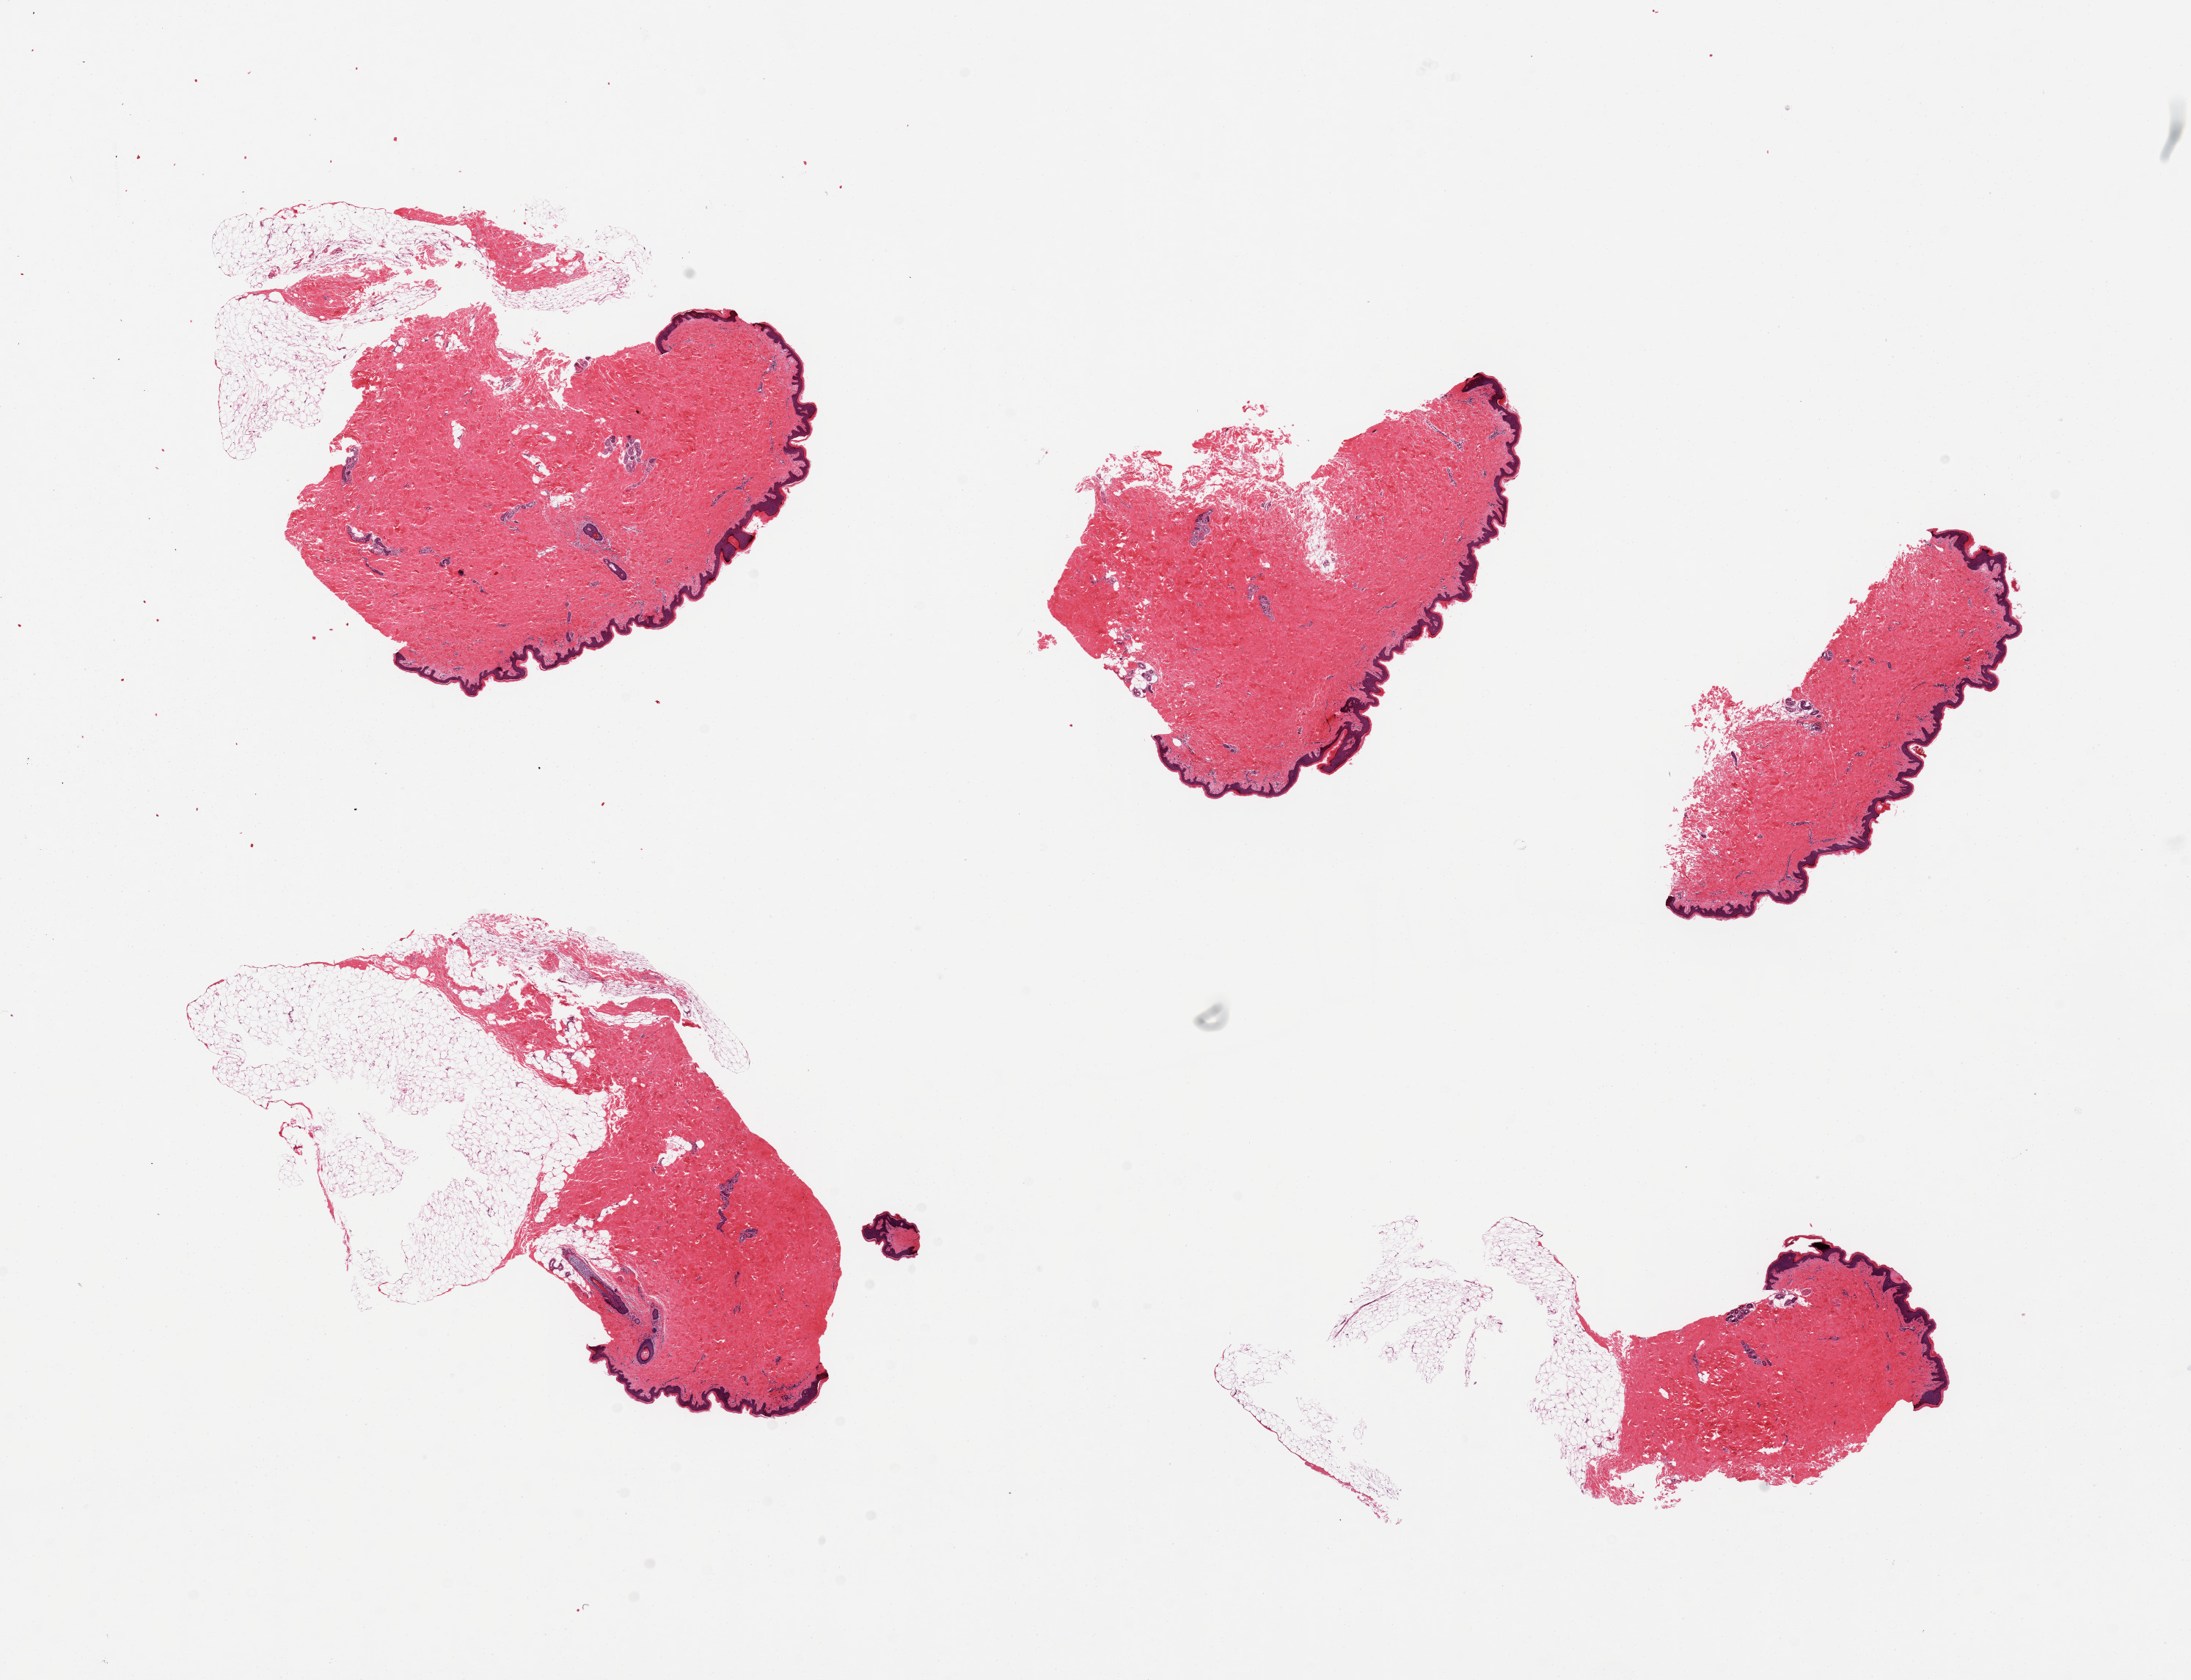
Digitized haematoxylin and eosin-stained section — low-resolution overview of the scanned area, about 23.6 x 18.1 mm (from a 20x scan), PAXgene-fixed paraffin-embedded (PFPE) section, target tissue: skin of suprapubic region, tissue donor sample. Donor sex: female.
Reviewer comment on this tissue sample: 5 pieces, 3 of 5 include significant attached fat from 30-50%.